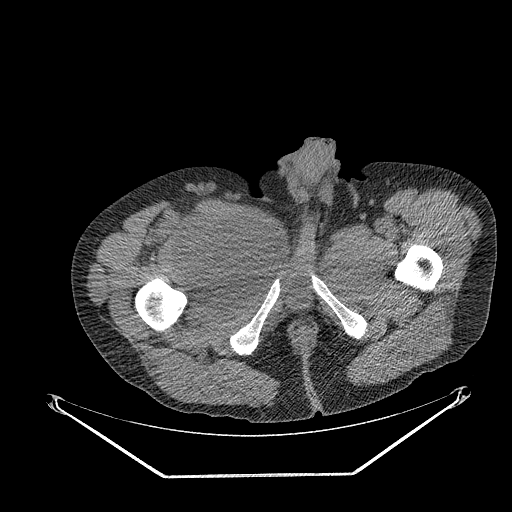
CT of an extremity soft-tissue mass (from a PET/CT study), one axial slice; position 286 of 311 along the scan axis; reconstruction kernel STANDARD; 140 kVp; soft-tissue window (W 400 / L 40 HU); 3.75 mm slice thickness; 512 × 512 image matrix, field of view 500 × 500 mm. Male patient. Case-level facts recorded for this patient, not image findings: histological type: undifferentiated - pleiomorphic; grade: high; site of the primary tumour: right thigh.
Structures marked on this image (expert contour drawn on MRI and transferred to this co-registered scan by the dataset authors):
- gross tumour volume including surrounding oedema: bounding box <196,205,259,271> (left, top, right, bottom; pixels)
- gross tumour volume (mass): <196,212,254,266>